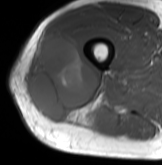
MRI of an extremity soft-tissue mass, one axial slice. Slice 40 of 61 in the series (ordered by position). MR volume resampled by the dataset authors to the PET/CT grid (not the native acquisition matrix). 162 × 165 image matrix. Male patient. From the clinical record (not read from this slice): histological type: poorly differentiated synovial sarcoma; grade: high; site of the primary tumour: right buttock.
Outlined on this slice (expert contour drawn on MRI and transferred to this co-registered scan by the dataset authors):
- gross tumour volume including surrounding oedema: bounding box <27,31,101,124> (left, top, right, bottom; pixels)
- gross tumour volume (mass): <30,31,99,121>